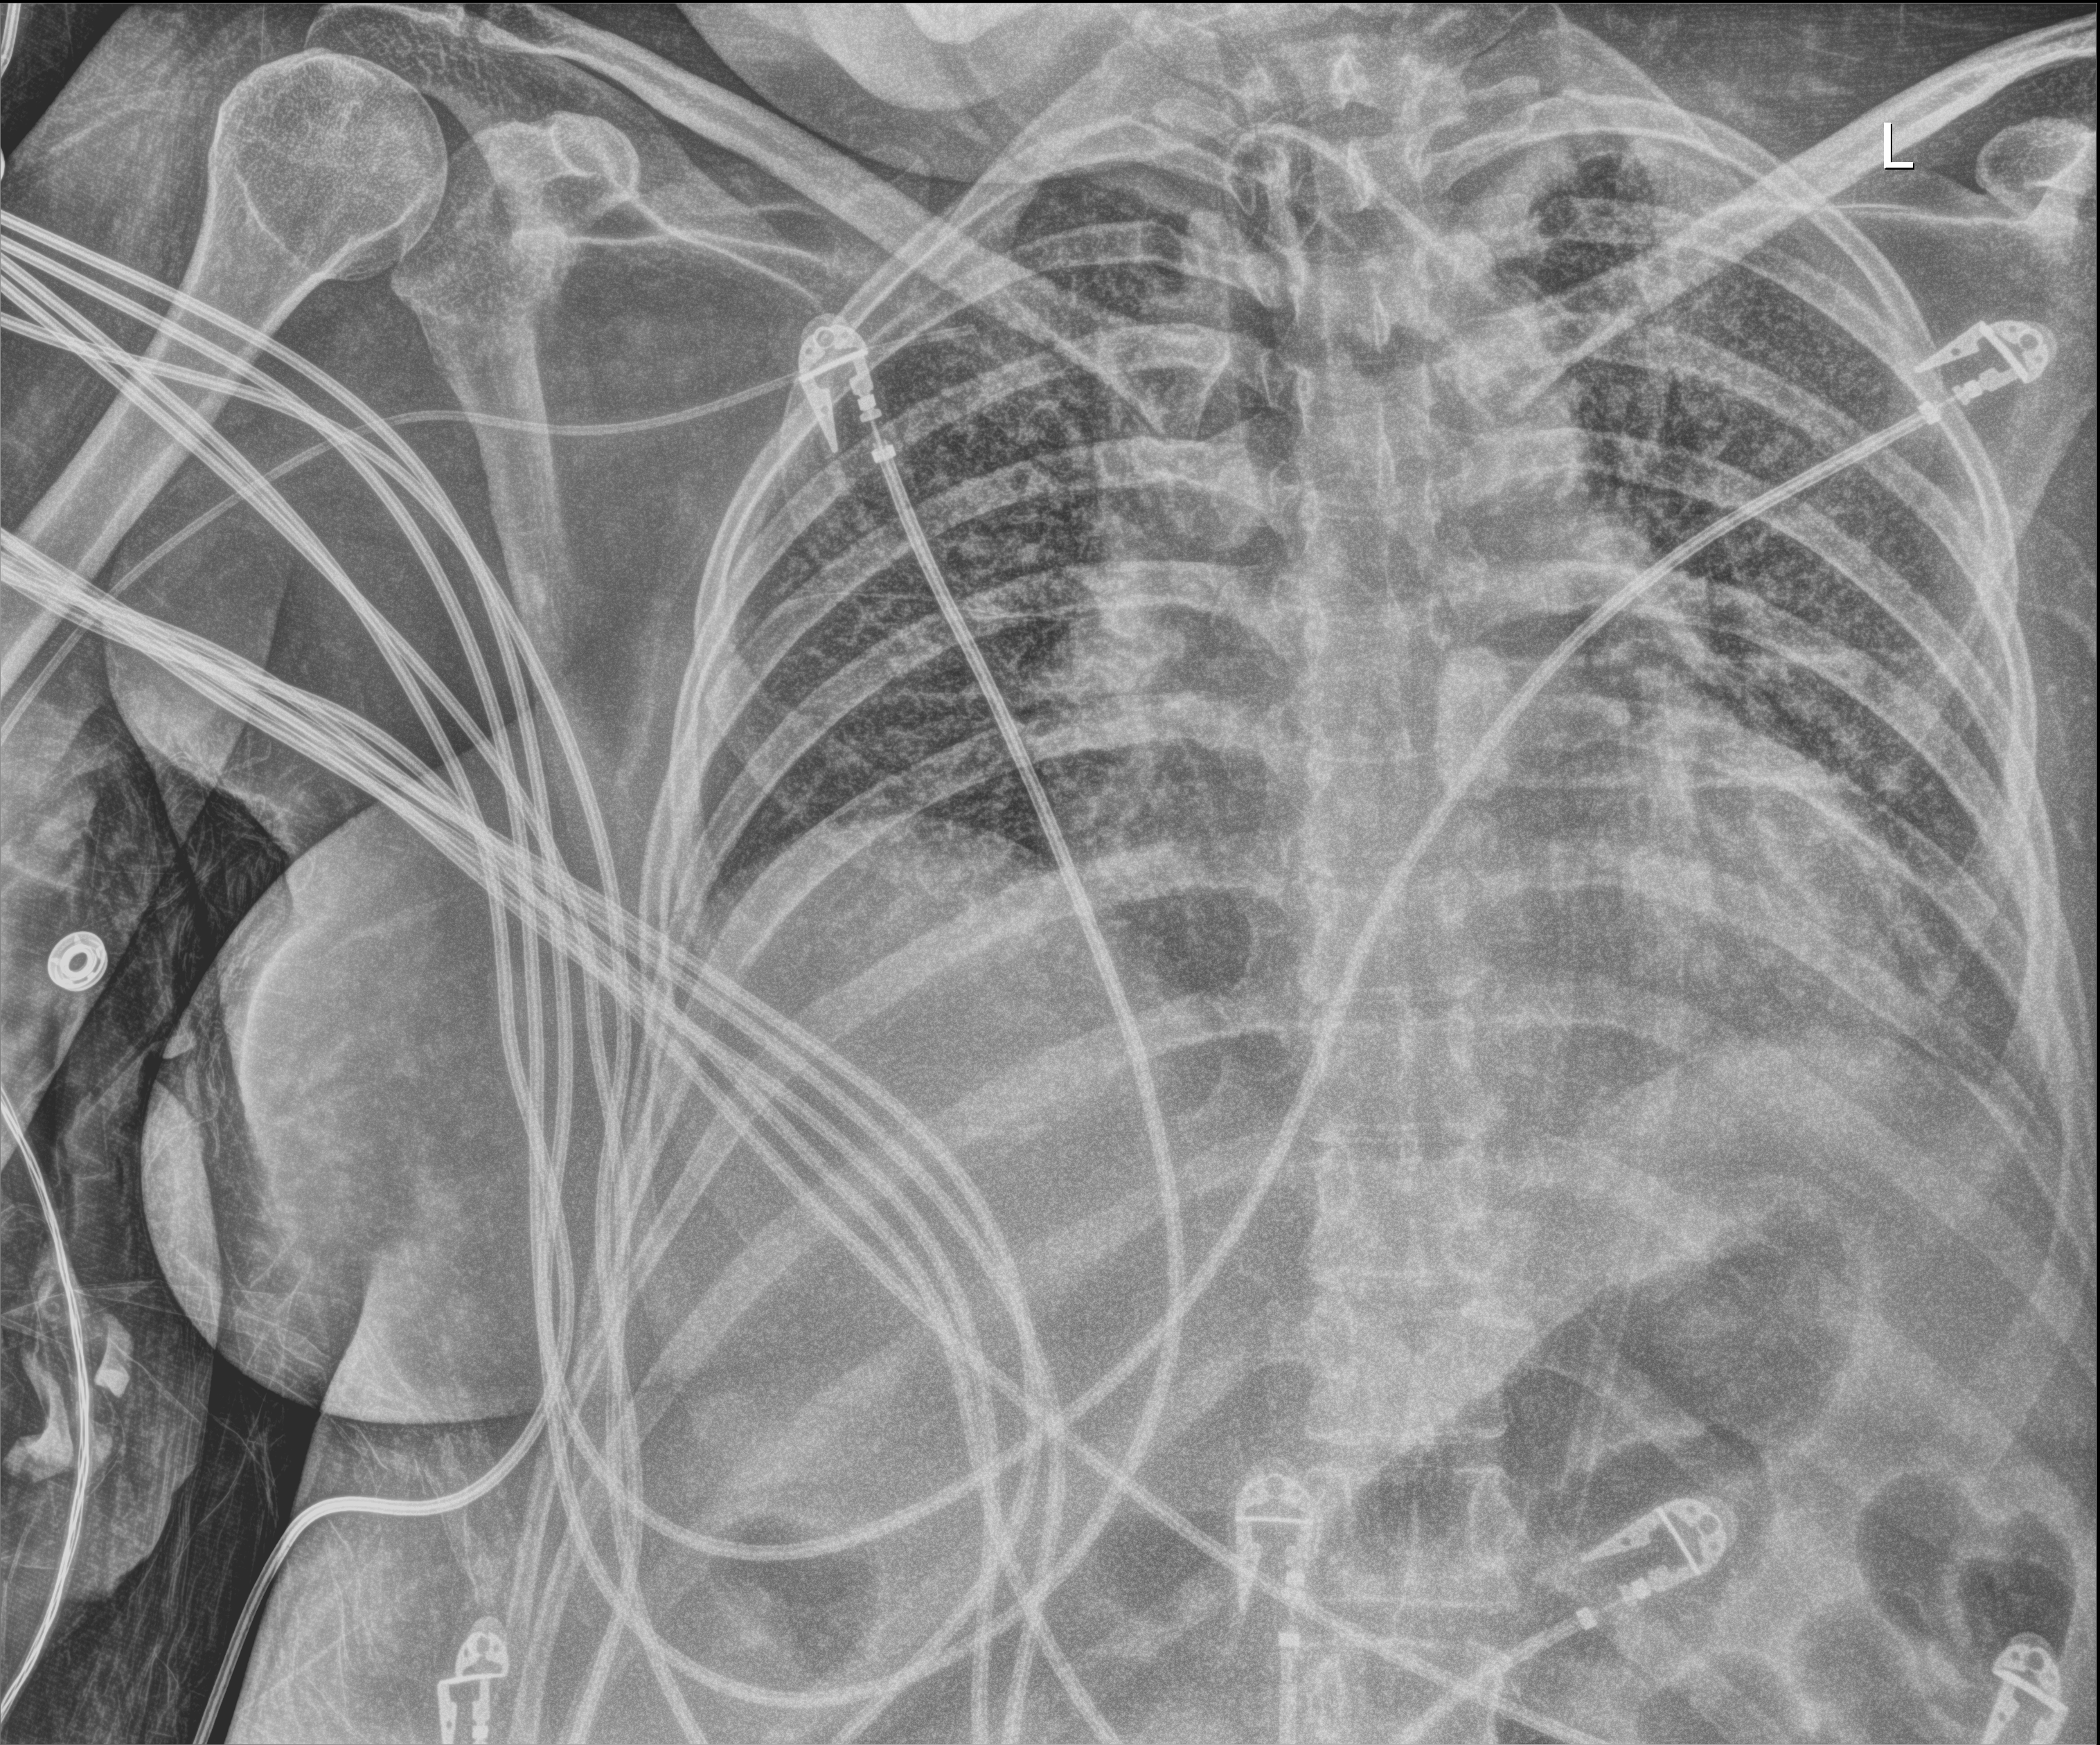
Chest X-ray (portable); anteroposterior (AP) projection. Female patient hospitalised with COVID-19, age 18–59 years.
Admission-level facts for this patient (not findings on this image; timing relative to this image not recorded):
- length of hospital stay: 73 days